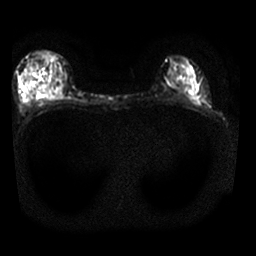
Breast MRI, one axial slice. Position 13 of 25 along the scan axis. Diffusion-weighted series; image 2 of 4 stored at this slice position (different b-values; order by instance number). 1.5 T. 4 mm slice thickness. 256 × 256 image matrix. Female patient.
Annotated regions visible in this slice (manually delineated by an expert):
- tumour on diffusion-weighted imaging: bounding box <42,86,61,90> (left, top, right, bottom; pixels)